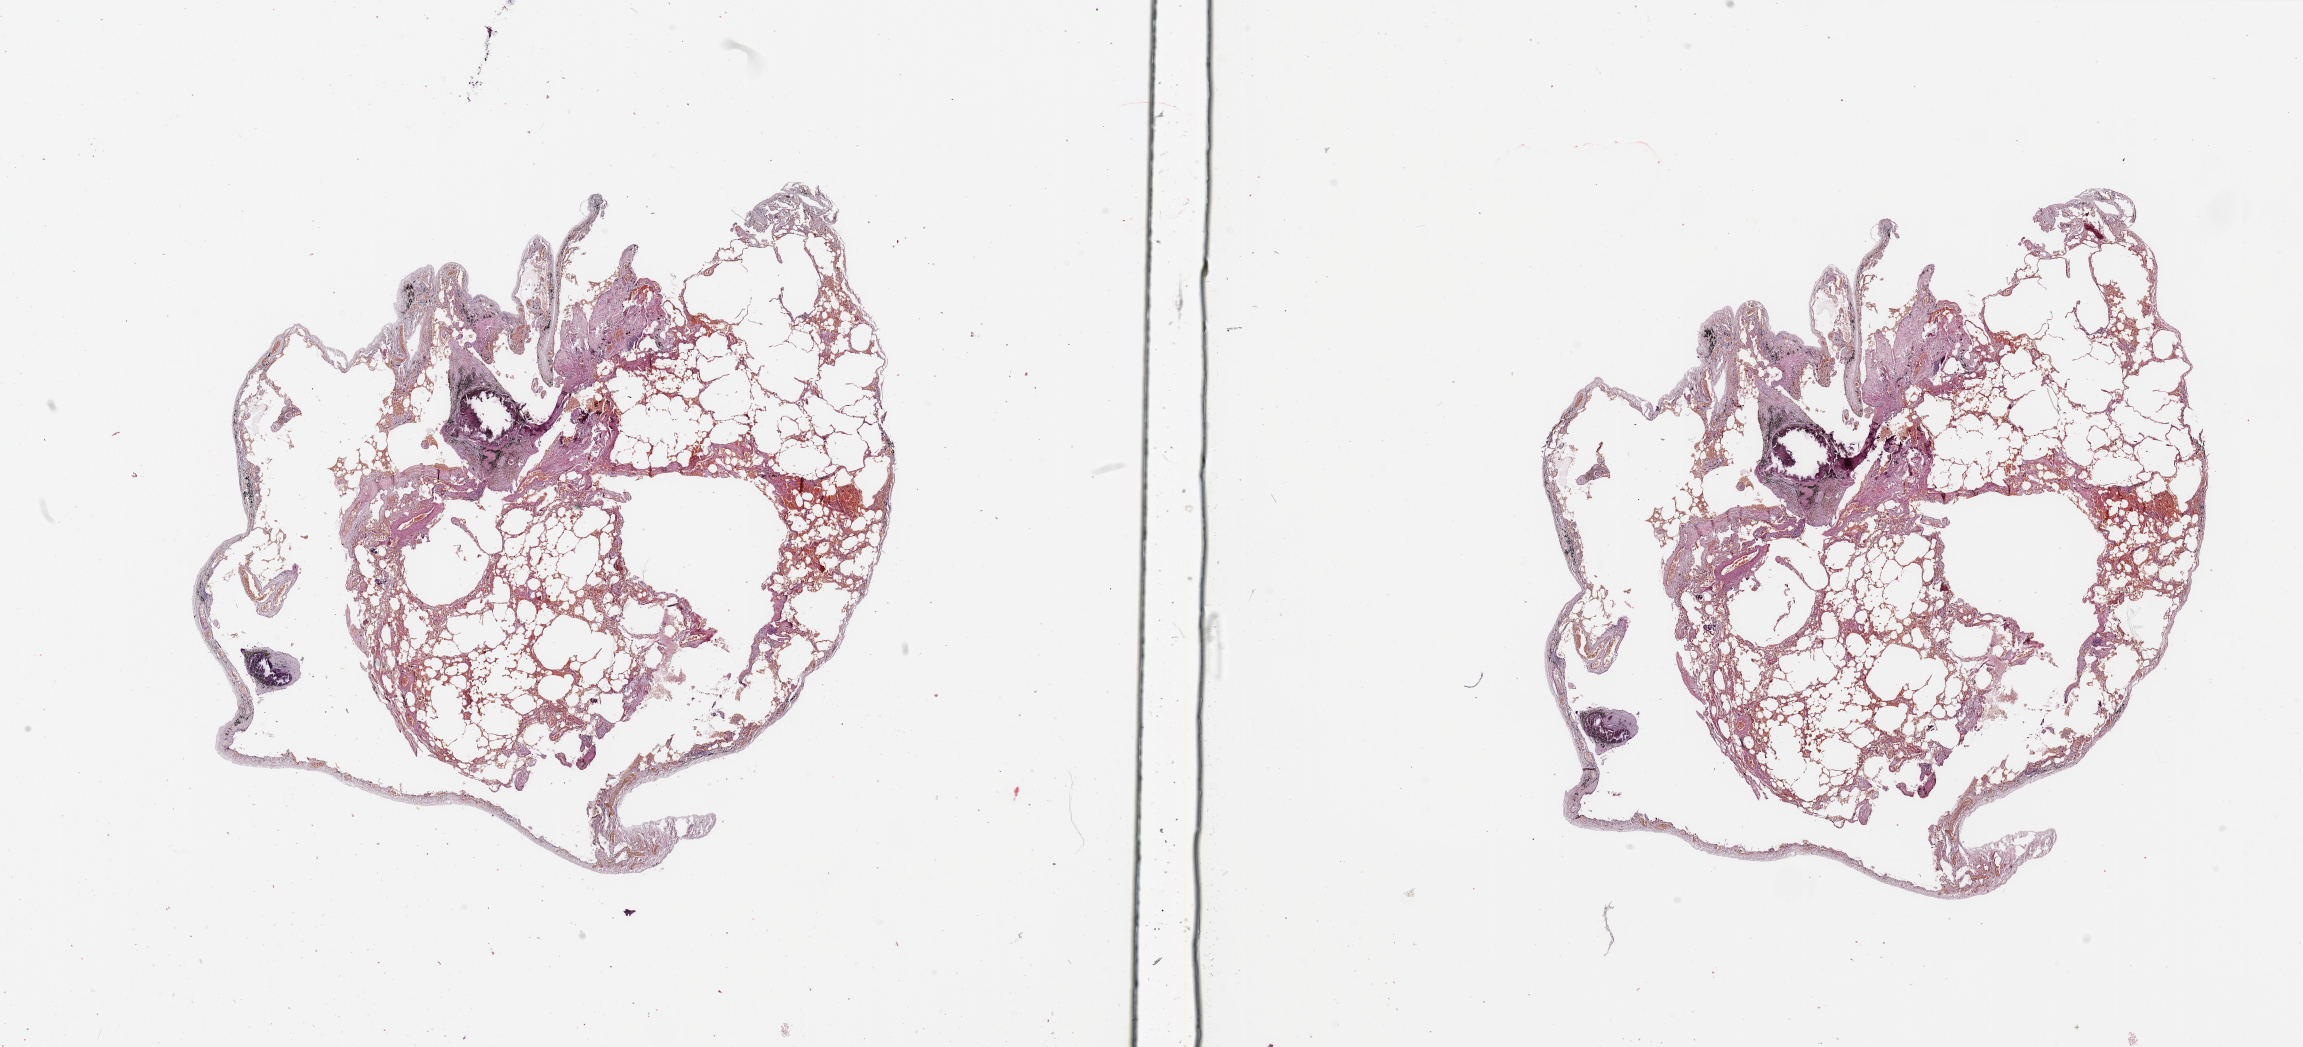
H&E whole-slide image, whole scanned area (about 36.4 x 16.6 mm) shown as a low-resolution overview, normal (non-tumour) tissue sample, sampled site: lung. Male, 69 y/o.
• this section: normal (non-tumour) tissue from the same patient
• patient diagnosis: Adenocarcinoma, NOS